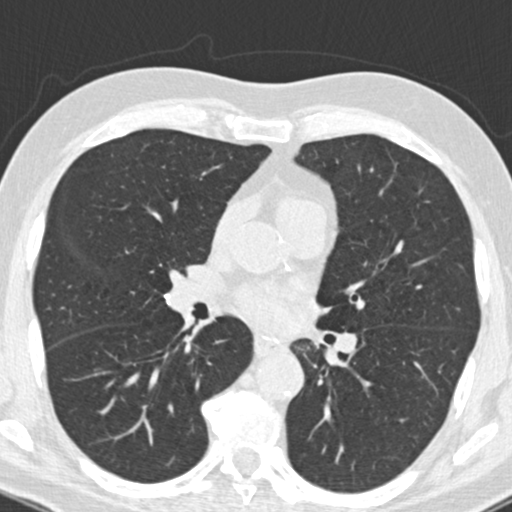
Low-dose screening chest CT, axial slice; second screening round (one year after baseline); lung window (W 1500 / L -600 HU); 2 mm slice thickness; slice 87 of 177 in the series; 512 × 512 image matrix, field of view 310 × 310 mm. Male, age 66 years at enrolment. Current smoker at enrolment.
Expert-annotated lung lesion, bounding box (x1, y1, x2, y2) in pixels: (182, 311, 210, 341). Screening reader's record for this exam (one nodule recorded; not confirmed to be the boxed lesion): non-calcified nodule or mass ≥4 mm, right upper lobe, 5 × 4 mm, smooth margins, pre-existing on the prior screen: yes; interval growth: no. Official screen result: positive, other.